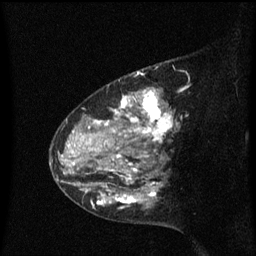
Breast MRI (dynamic contrast-enhanced), one sagittal slice; slice 42 of 60 in the series (ordered by position); dynamic contrast-enhanced series, image 2 of 3 at this slice position (ordered by acquisition); 1.5 T; TE 4.2 ms, TR 8.4 ms; 256 × 256 image matrix. Female patient, age 48 years. Case-level facts recorded for this patient, not image findings: setting: breast cancer imaged before/during neoadjuvant chemotherapy; receptor status: HR-positive, HER2-negative.
Structures marked on this image (semi-automatic segmentation, software-assisted and operator-edited):
- analysis volume of interest (the breast-tissue region the enhancement analysis was run in; not a lesion): bounding box (x1, y1, x2, y2) in pixels: (80, 78, 179, 217)
- tumour enhancement mask (voxels above the 70 % enhancement threshold inside the analysis volume of interest): (80, 89, 173, 209)